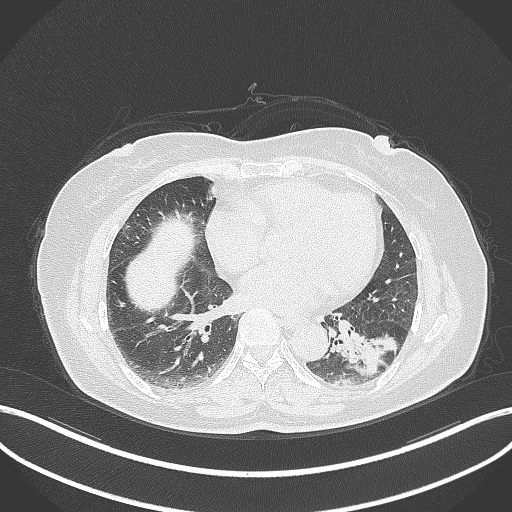
Chest CT, one axial slice. Slice 153 of 311 in the series (ordered by position). Reconstruction kernel B70f. 120 kVp. Lung window (W 1500 / L -600 HU). 1 mm slice thickness. 512 × 512 image matrix, field of view 400 × 400 mm. Patient: female, 59 years. Case-level facts recorded for this patient, not image findings: clinical TNM (as recorded): T2a N0 M0; histopathological grade: G2-3.
Annotated regions visible in this slice (bounding box drawn by a radiologist):
- lung tumour (recorded histology: adenocarcinoma): bounding box (x1, y1, x2, y2) in pixels: (344, 320, 401, 381)